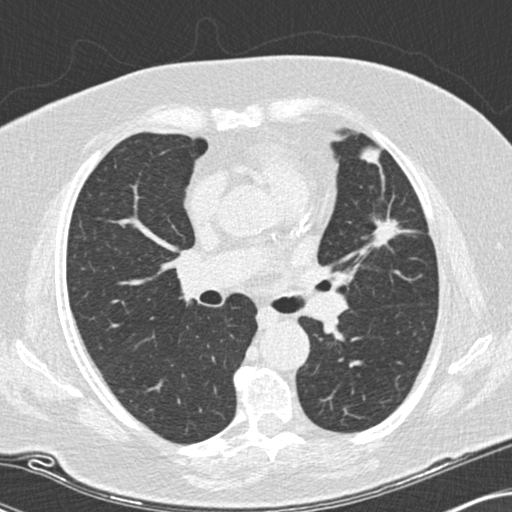
Low-dose screening chest CT, one axial slice. Slice 94 of 151 in the series (ordered by position). Reconstruction kernel B30f. Lung window (W 1500 / L -600 HU). 2 mm slice thickness. 512 × 512 image matrix, field of view 330 × 330 mm.
Outlined on this slice (manually delineated by an expert):
- lesion 1 (tumor, upper lobe of left lung): bounding box <368,217,402,248> (left, top, right, bottom; pixels)